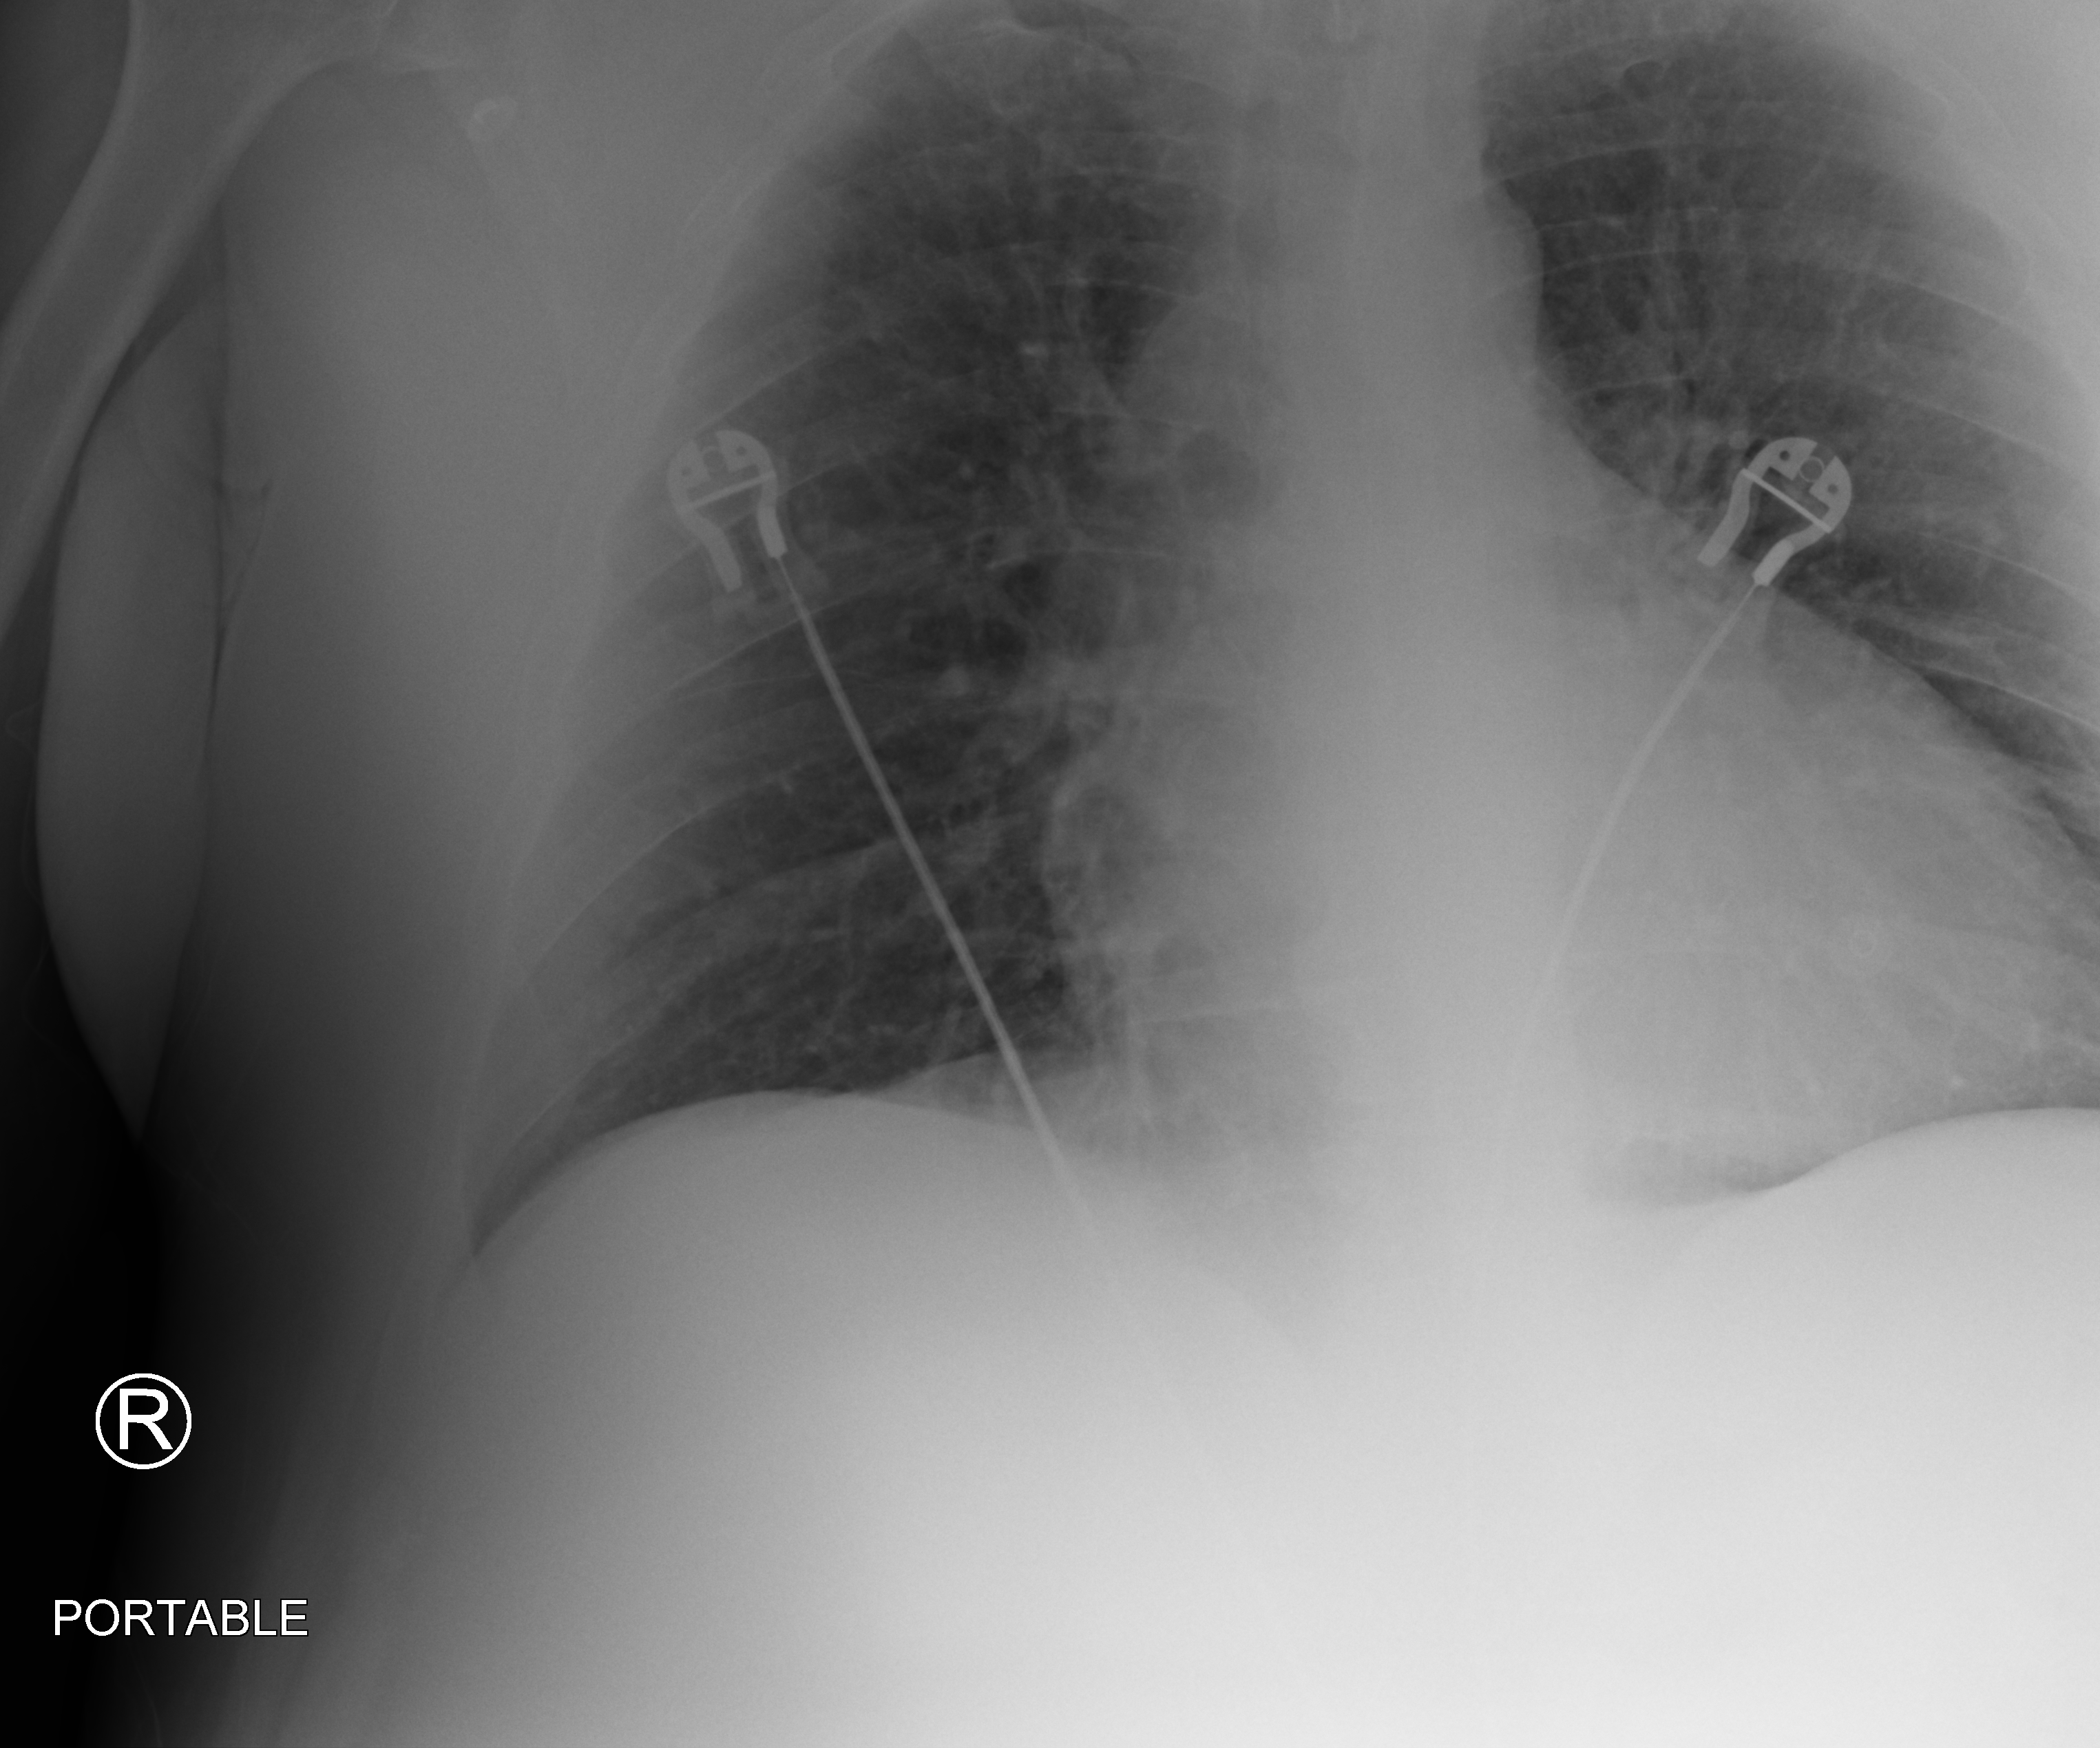
Bedside chest radiograph (computed radiography), anteroposterior (AP) projection. Male patient hospitalised with COVID-19, age 18–59 years.
From the hospital-stay record, not from the radiograph (when in the stay this image was taken is not recorded):
- hypertension (admission record): yes
- diabetes (admission record): no
- mechanically ventilated during this hospital stay: no